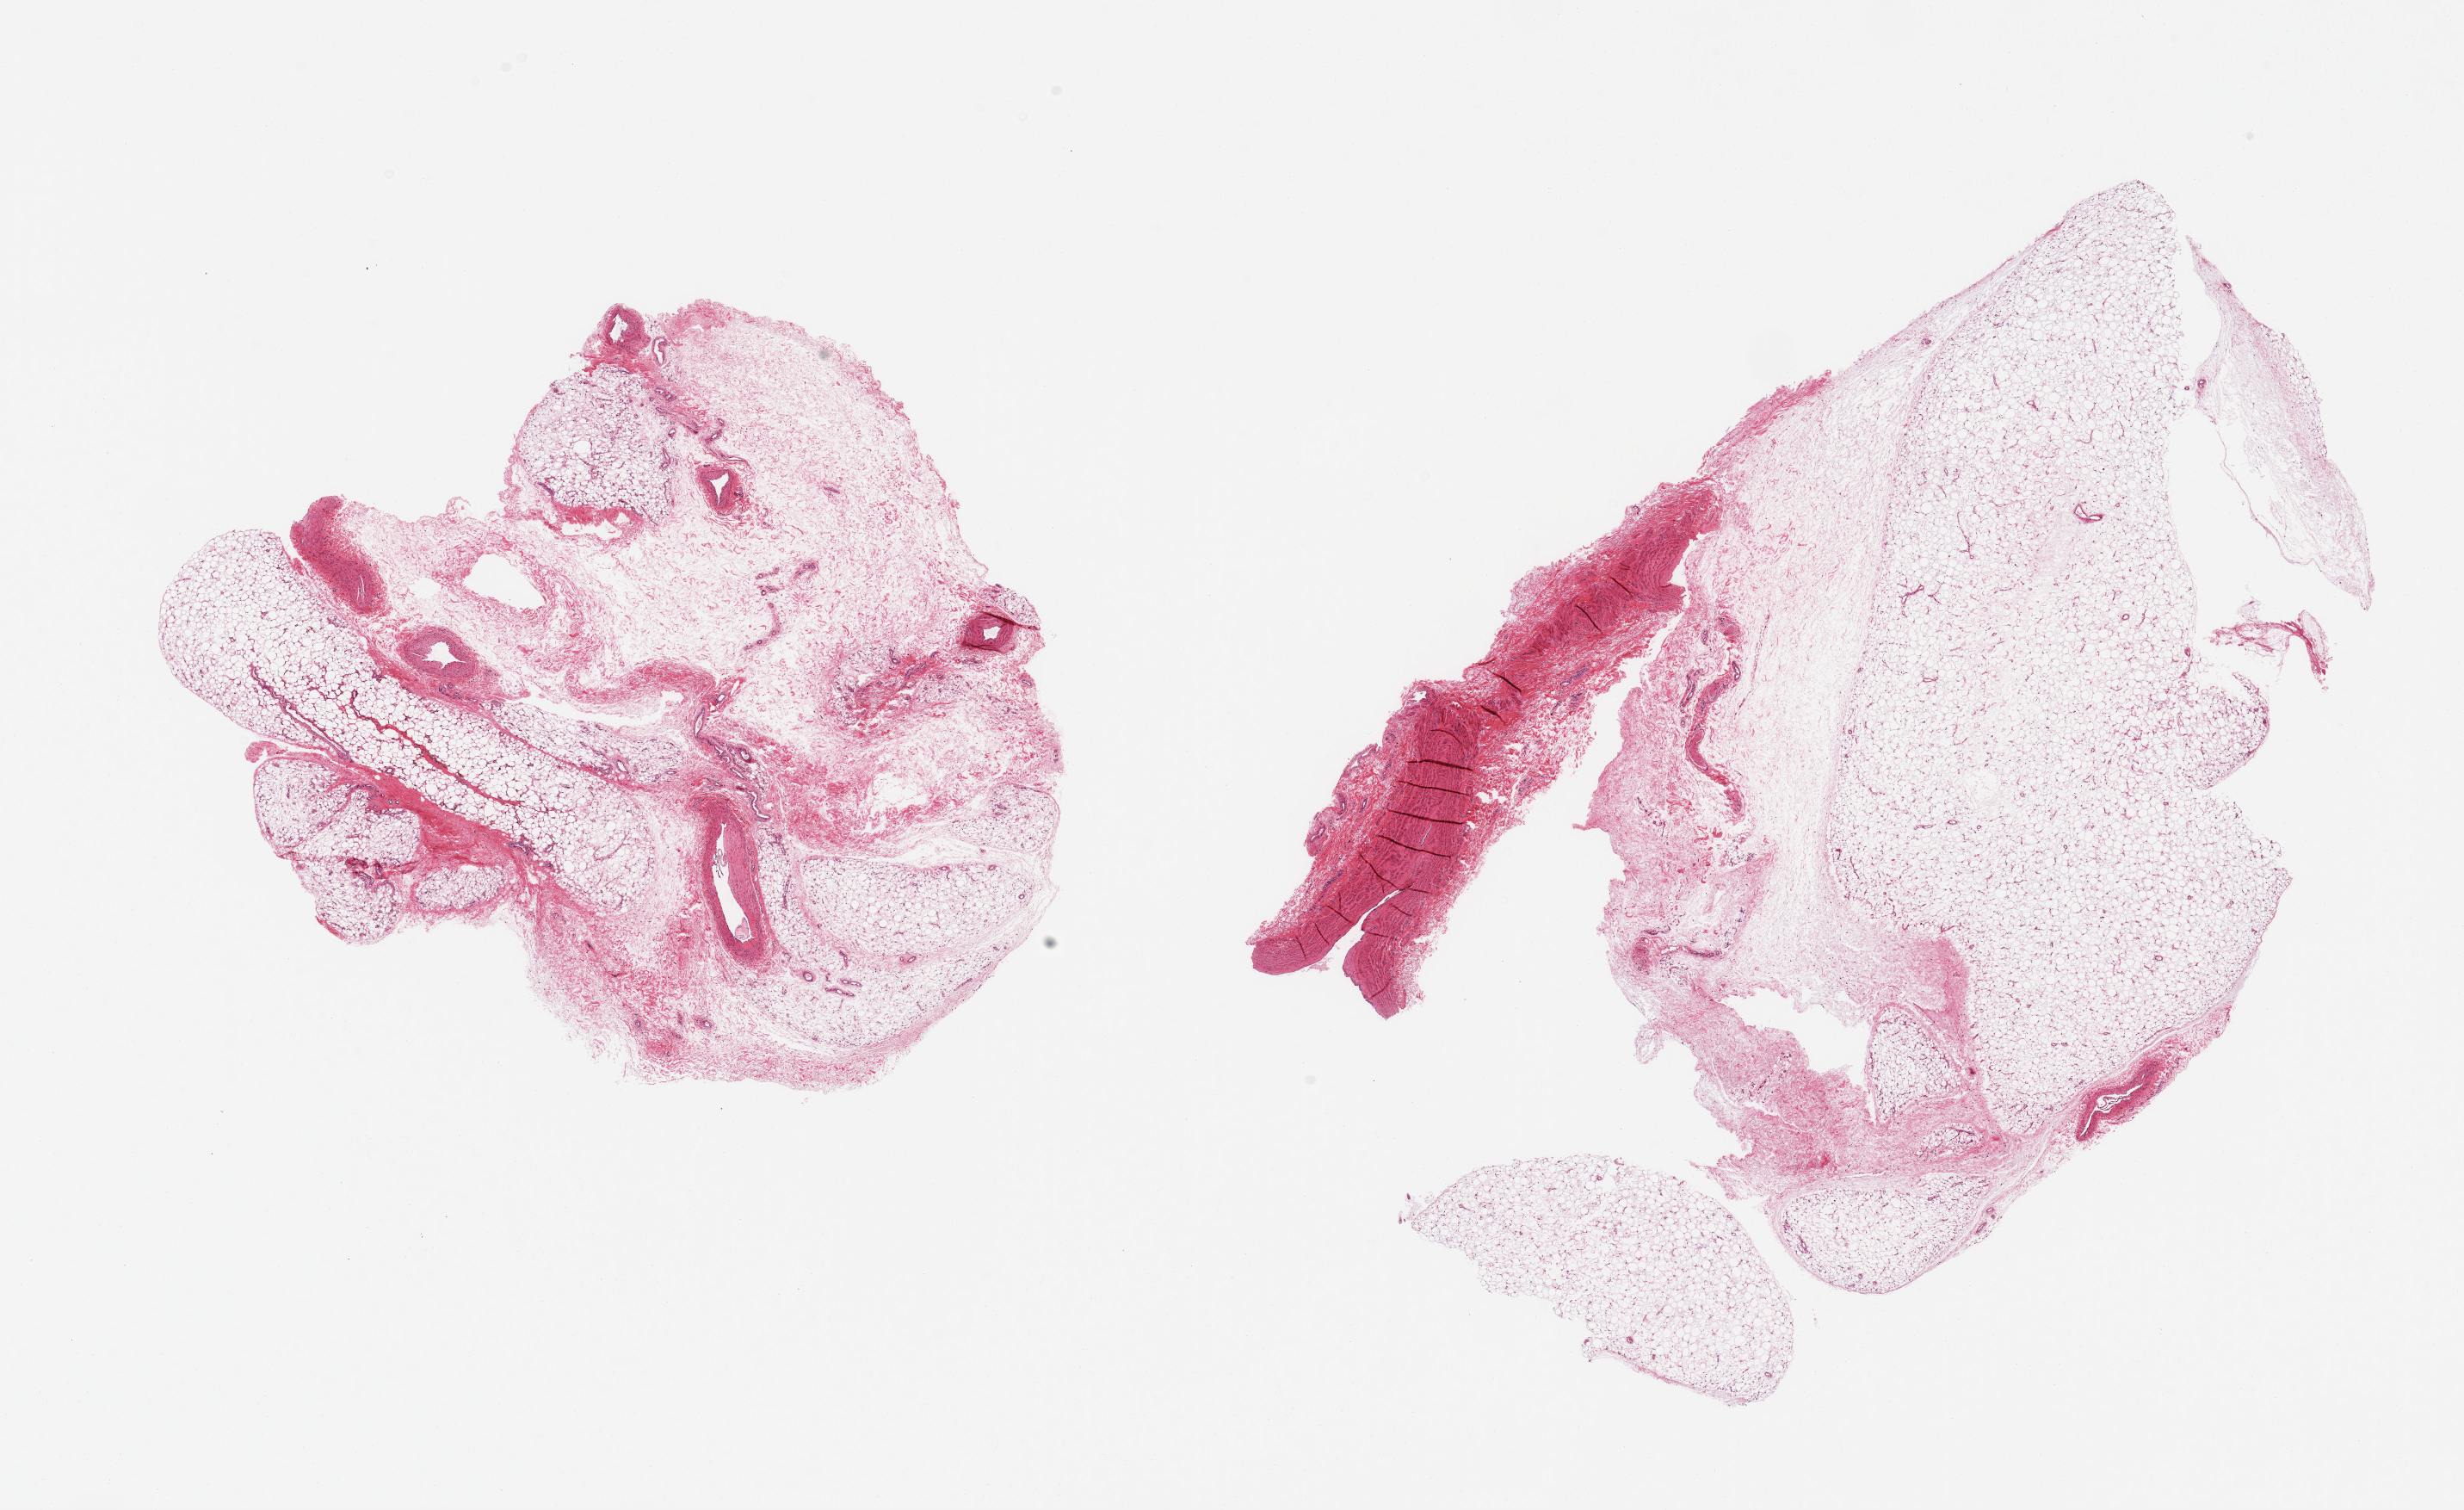
Whole-slide image, hematoxylin and eosin (H&E) stain, a low-resolution overview of the entire scanned area, about 22.6 x 13.9 mm (from a 20x scan). PAXgene-fixed paraffin-embedded (PFPE) section. Sampled site (target tissue): adipose tissue. Donor tissue sample. Male donor.
Review note (as recorded): 2 pieces; 10% vascular content.